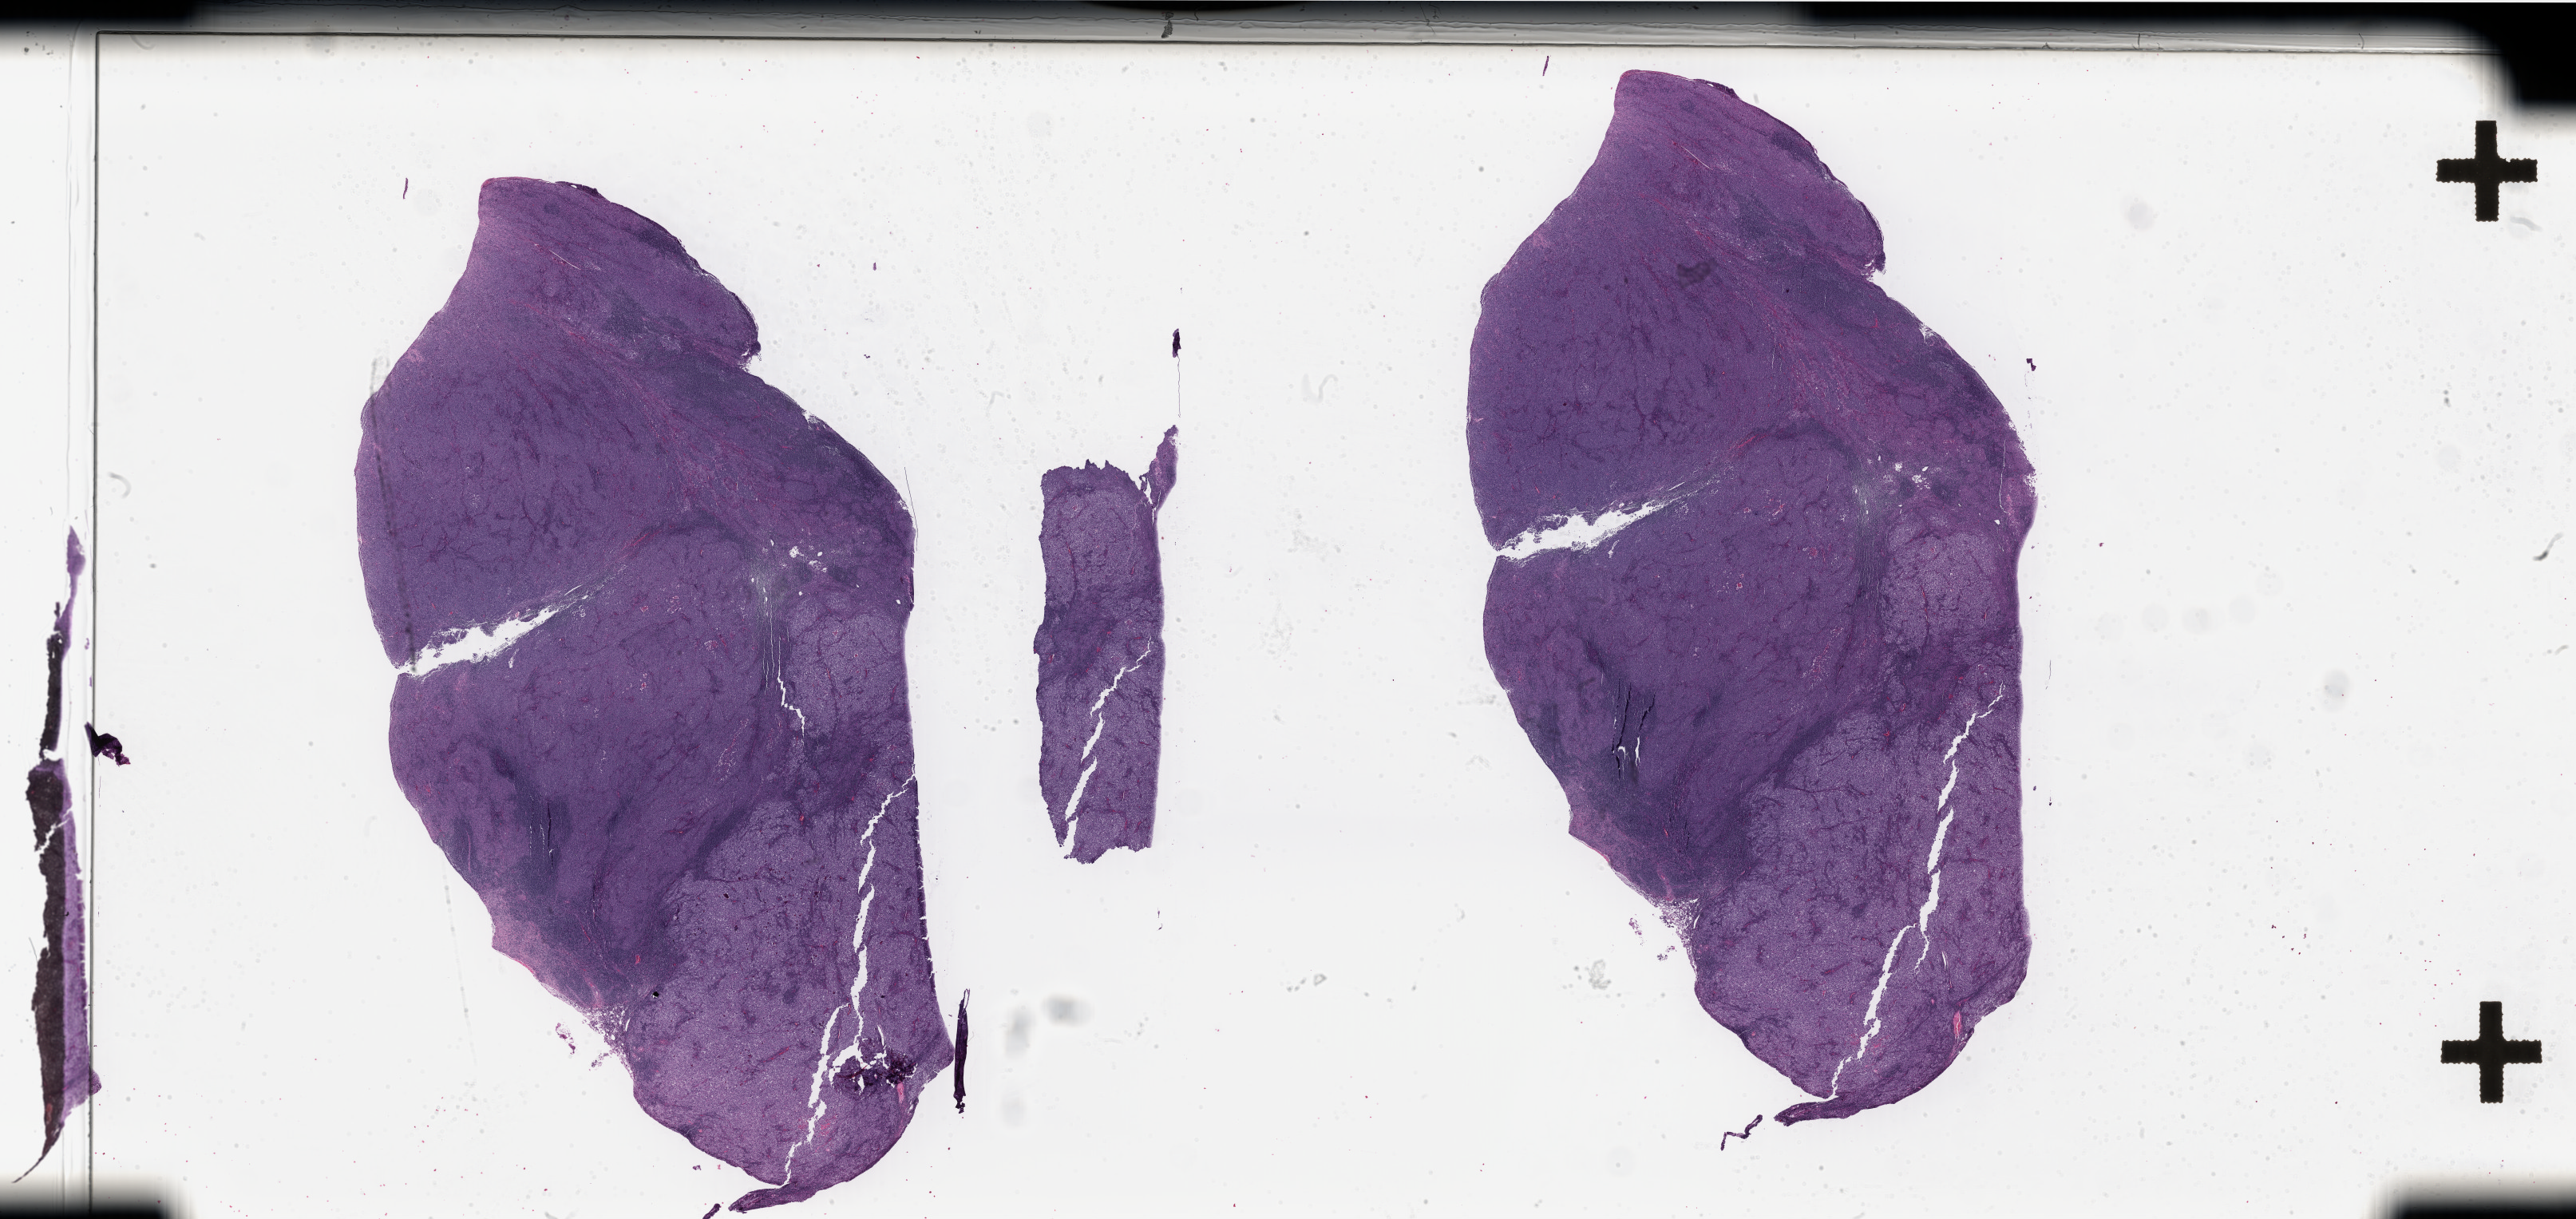
Whole-slide histology image, H&E, a low-resolution overview of the entire scanned area, about 51.1 x 24.2 mm (from a 40x scan), formalin-fixed paraffin-embedded (FFPE) diagnostic section, sample: primary tumour, skin. Female, age 38 years at initial diagnosis.
Diagnosis: Malignant melanoma, NOS.